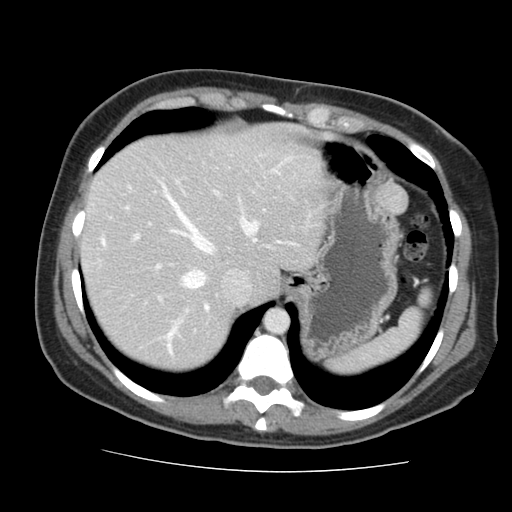
Contrast-enhanced abdominal CT, one axial slice. Slice 120 of 144 in the series (ordered by position). 120 kVp. Intravenous contrast given. Soft-tissue window (W 400 / L 40 HU). 512 × 512 image matrix, field of view 333 × 333 mm. Female patient, age 46 years. Case-level facts recorded for this patient, not image findings: diagnosis: colorectal cancer liver metastases, imaged before liver resection; multiple liver metastases: no; largest metastasis: 2.8 cm.
Outlined on this slice (outlined manually by an expert reader):
- hepatic veins: bounding box (x1, y1, x2, y2) in pixels: (160, 182, 317, 341)
- liver: (83, 127, 326, 369)
- planned liver remnant (the part of the liver to remain after resection): (83, 127, 326, 369)
- portal vein (with intrahepatic branches): (102, 181, 218, 353)